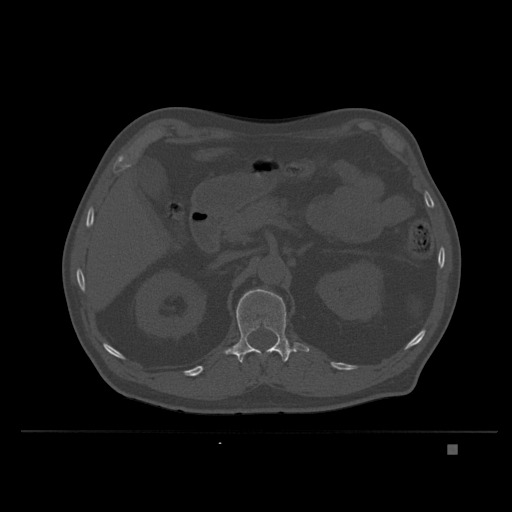
CT including the spine, one axial slice; position 141 of 435 along the scan axis; bone window (W 1800 / L 400 HU); 1.5 mm slice thickness; 512 × 512 image matrix. Male patient, age 73 years. From the clinical record (not read from this slice): primary cancer: skin.
Outlined on this slice (semi-automatically segmented with operator editing):
- L1 vertebra: bounding box (x1, y1, x2, y2) in pixels: (224, 289, 310, 363)